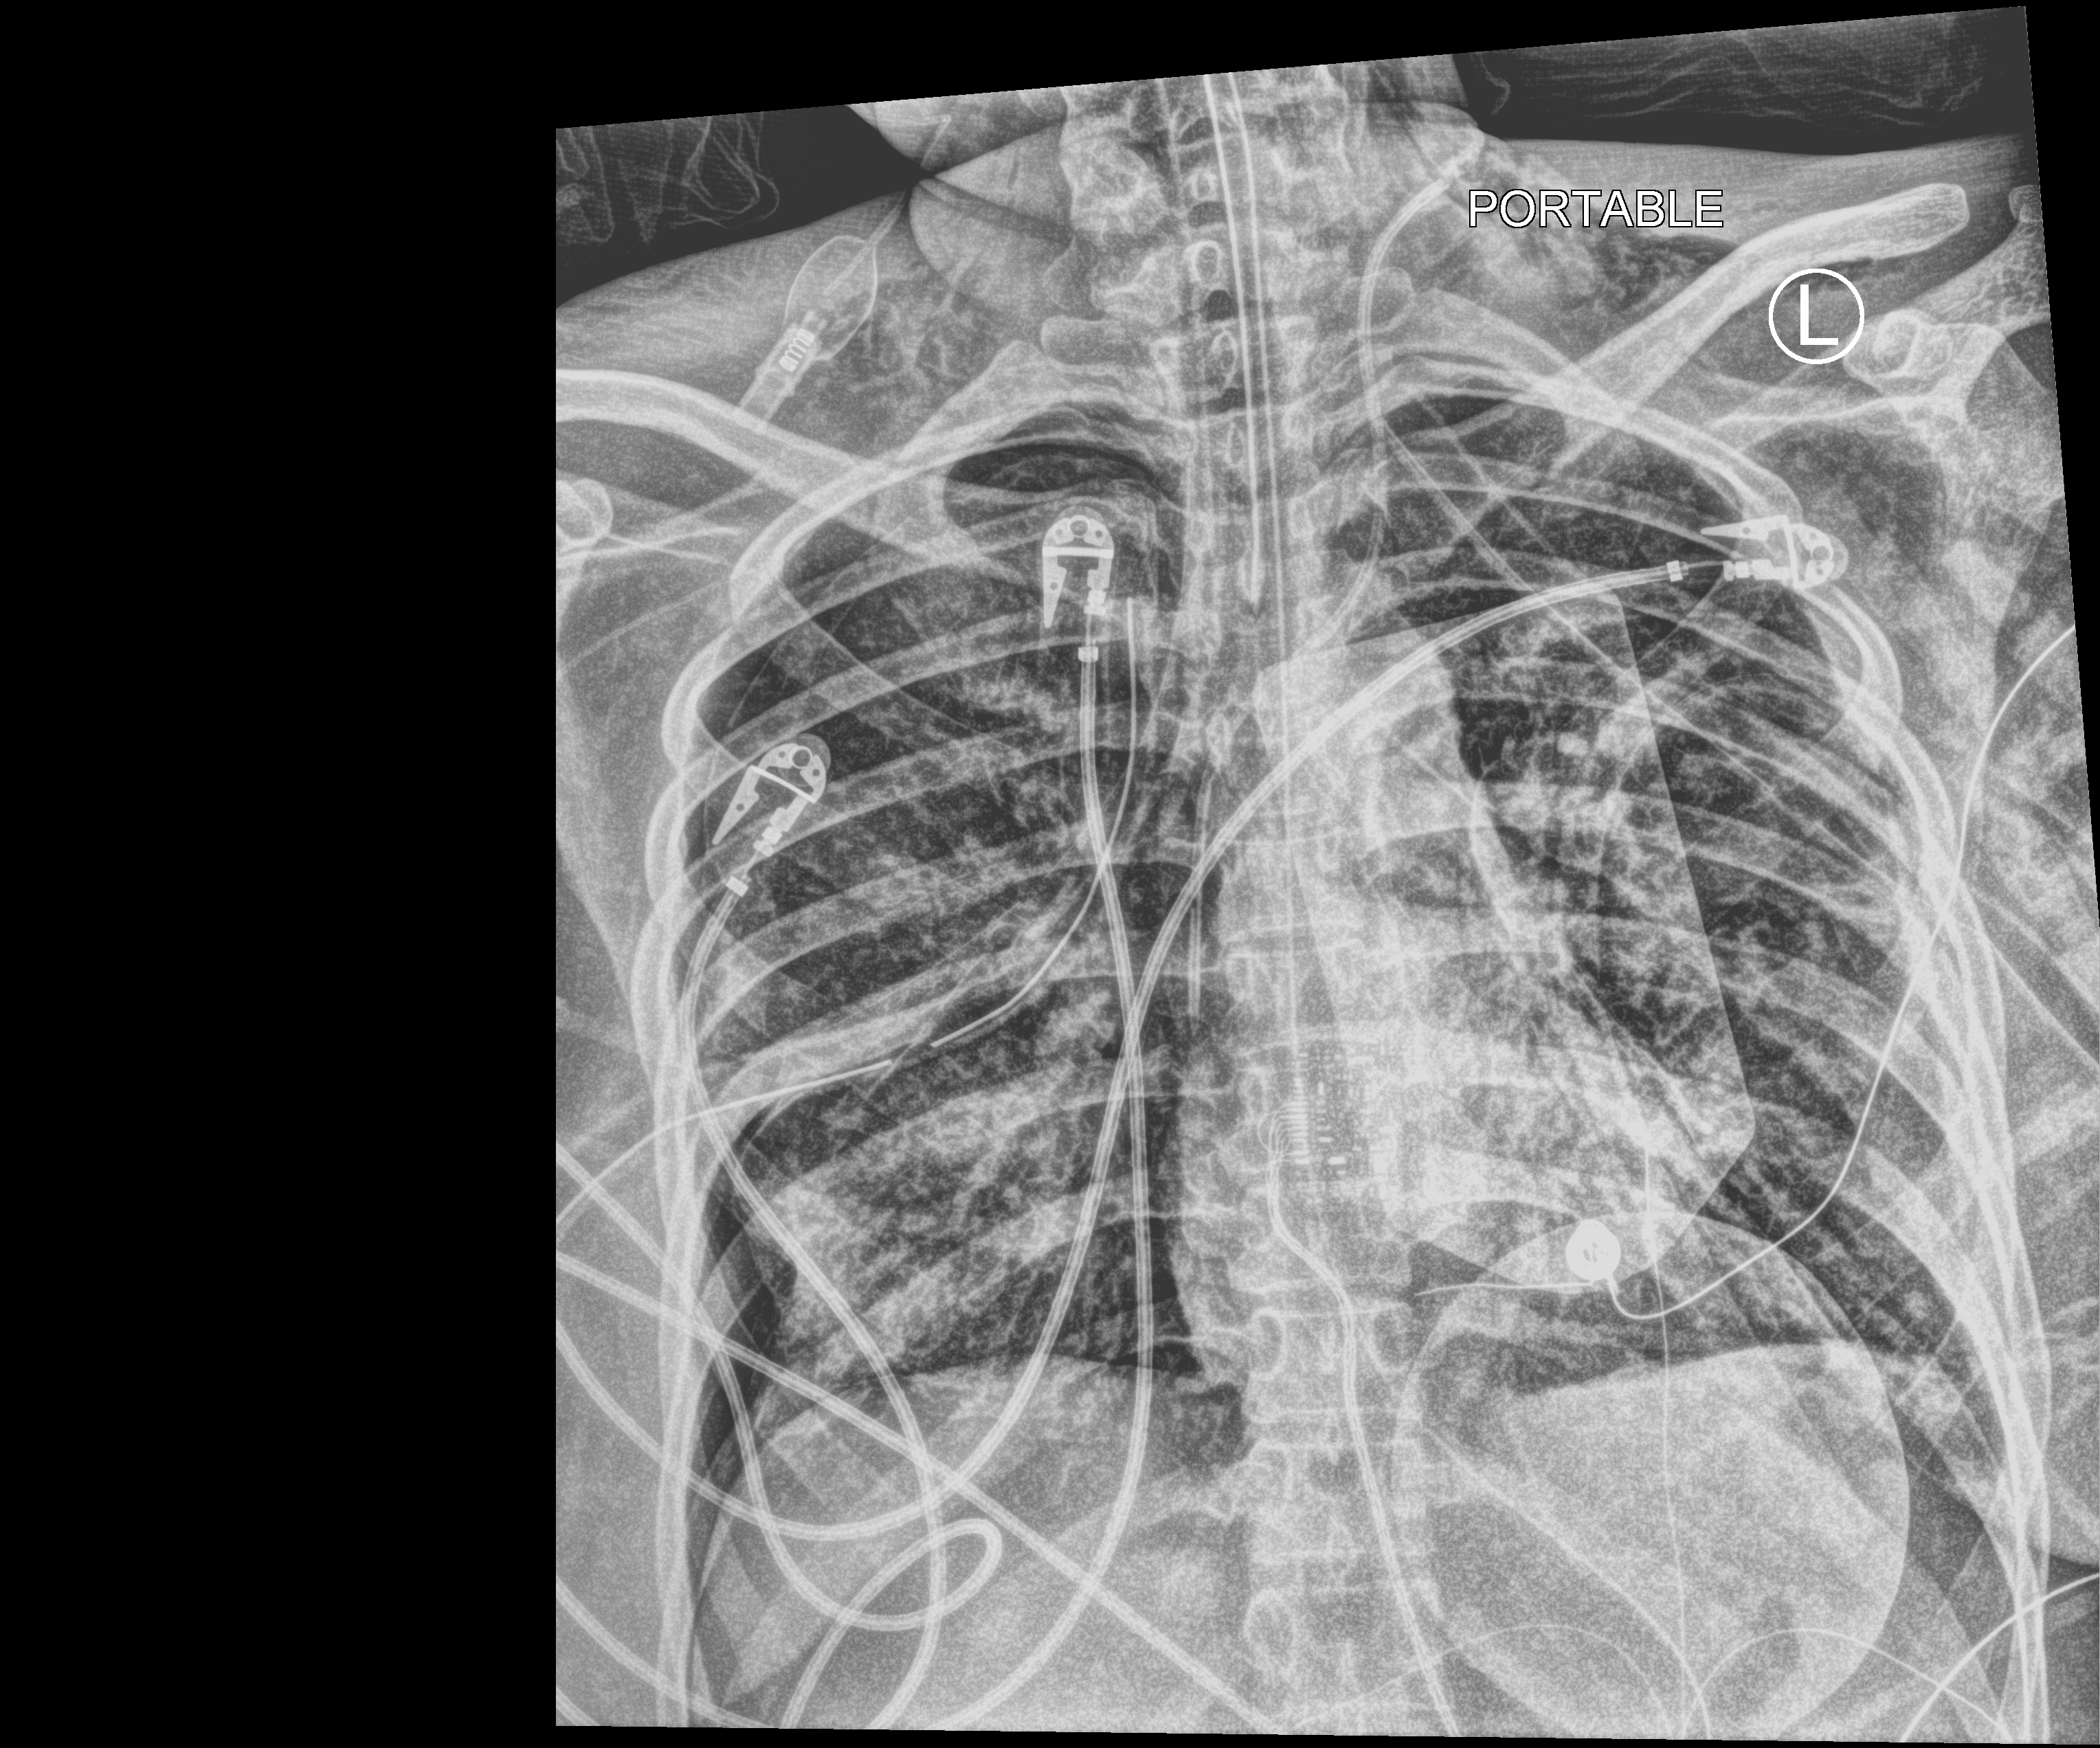
Bedside chest radiograph (computed radiography); anteroposterior (AP) projection. Patient hospitalised with COVID-19, aged 18–59 years.
Hospital-stay facts (about this admission, not read from this image; timing relative to this image not recorded):
- chronic kidney disease (admission record): no
- mechanically ventilated during this hospital stay: yes